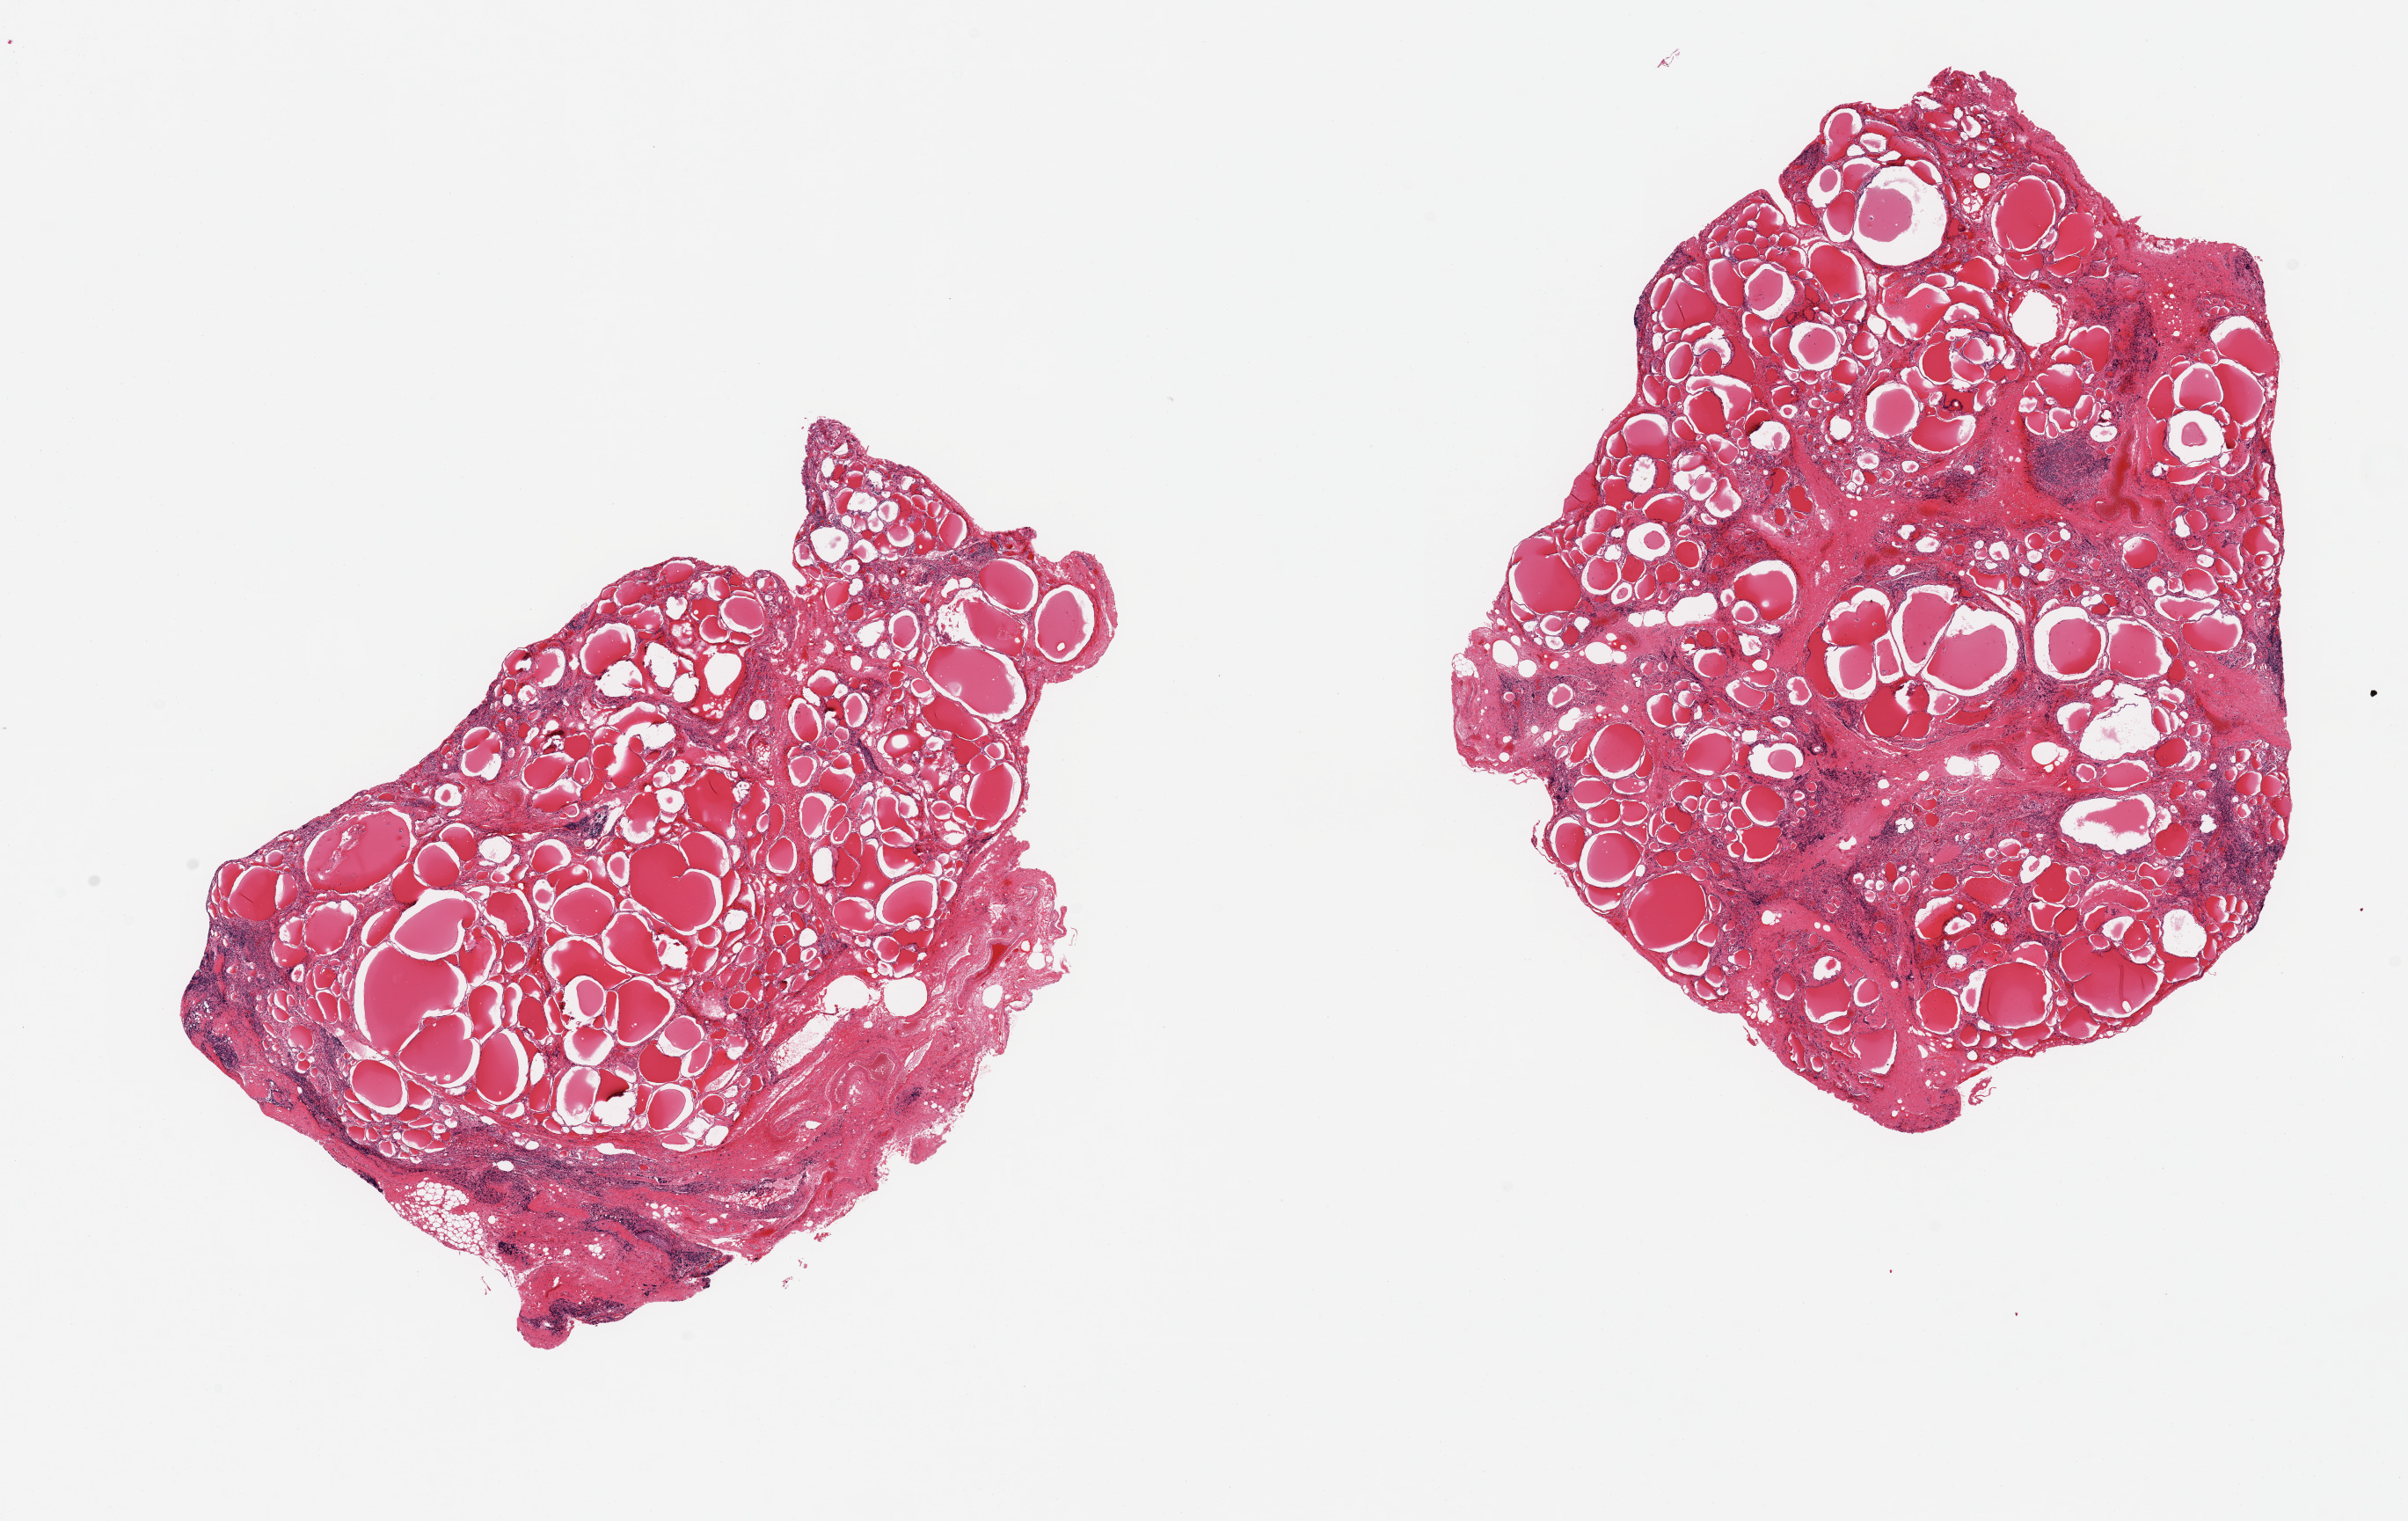
Haematoxylin and eosin whole-slide image — whole scanned area (about 21.7 x 13.7 mm, slide scanned at 20x) shown as a low-resolution overview, PAXgene-fixed, paraffin-embedded tissue, target tissue: thyroid, tissue donor sample. Donor sex: male.
- review note (as recorded): 2 pieces; Nodular goiter; lymphocytic/Hashimoto thyroiditis, lymphoid aggregates